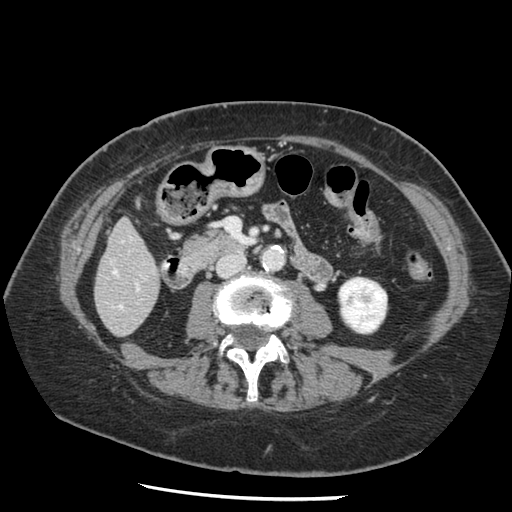
Contrast-enhanced abdominal CT, one axial slice. Slice 36 of 148 in the series (ordered by position). Reconstruction kernel STANDARD. 120 kVp. Intravenous contrast given. Soft-tissue window (W 400 / L 40 HU). 2.5 mm slice thickness. 512 × 512 image matrix, field of view 330 × 330 mm. Female patient, age 85 years. Case-level facts recorded for this patient, not image findings: diagnosis: colorectal cancer liver metastases, imaged before liver resection; multiple liver metastases: no; largest metastasis: 0.9 cm.
Structures marked on this image (outlined manually by an expert reader):
- hepatic veins: bounding box [x1, y1, x2, y2] px = [113, 270, 121, 308]
- liver: [96, 221, 160, 335]
- planned liver remnant (the part of the liver to remain after resection): [96, 221, 160, 332]